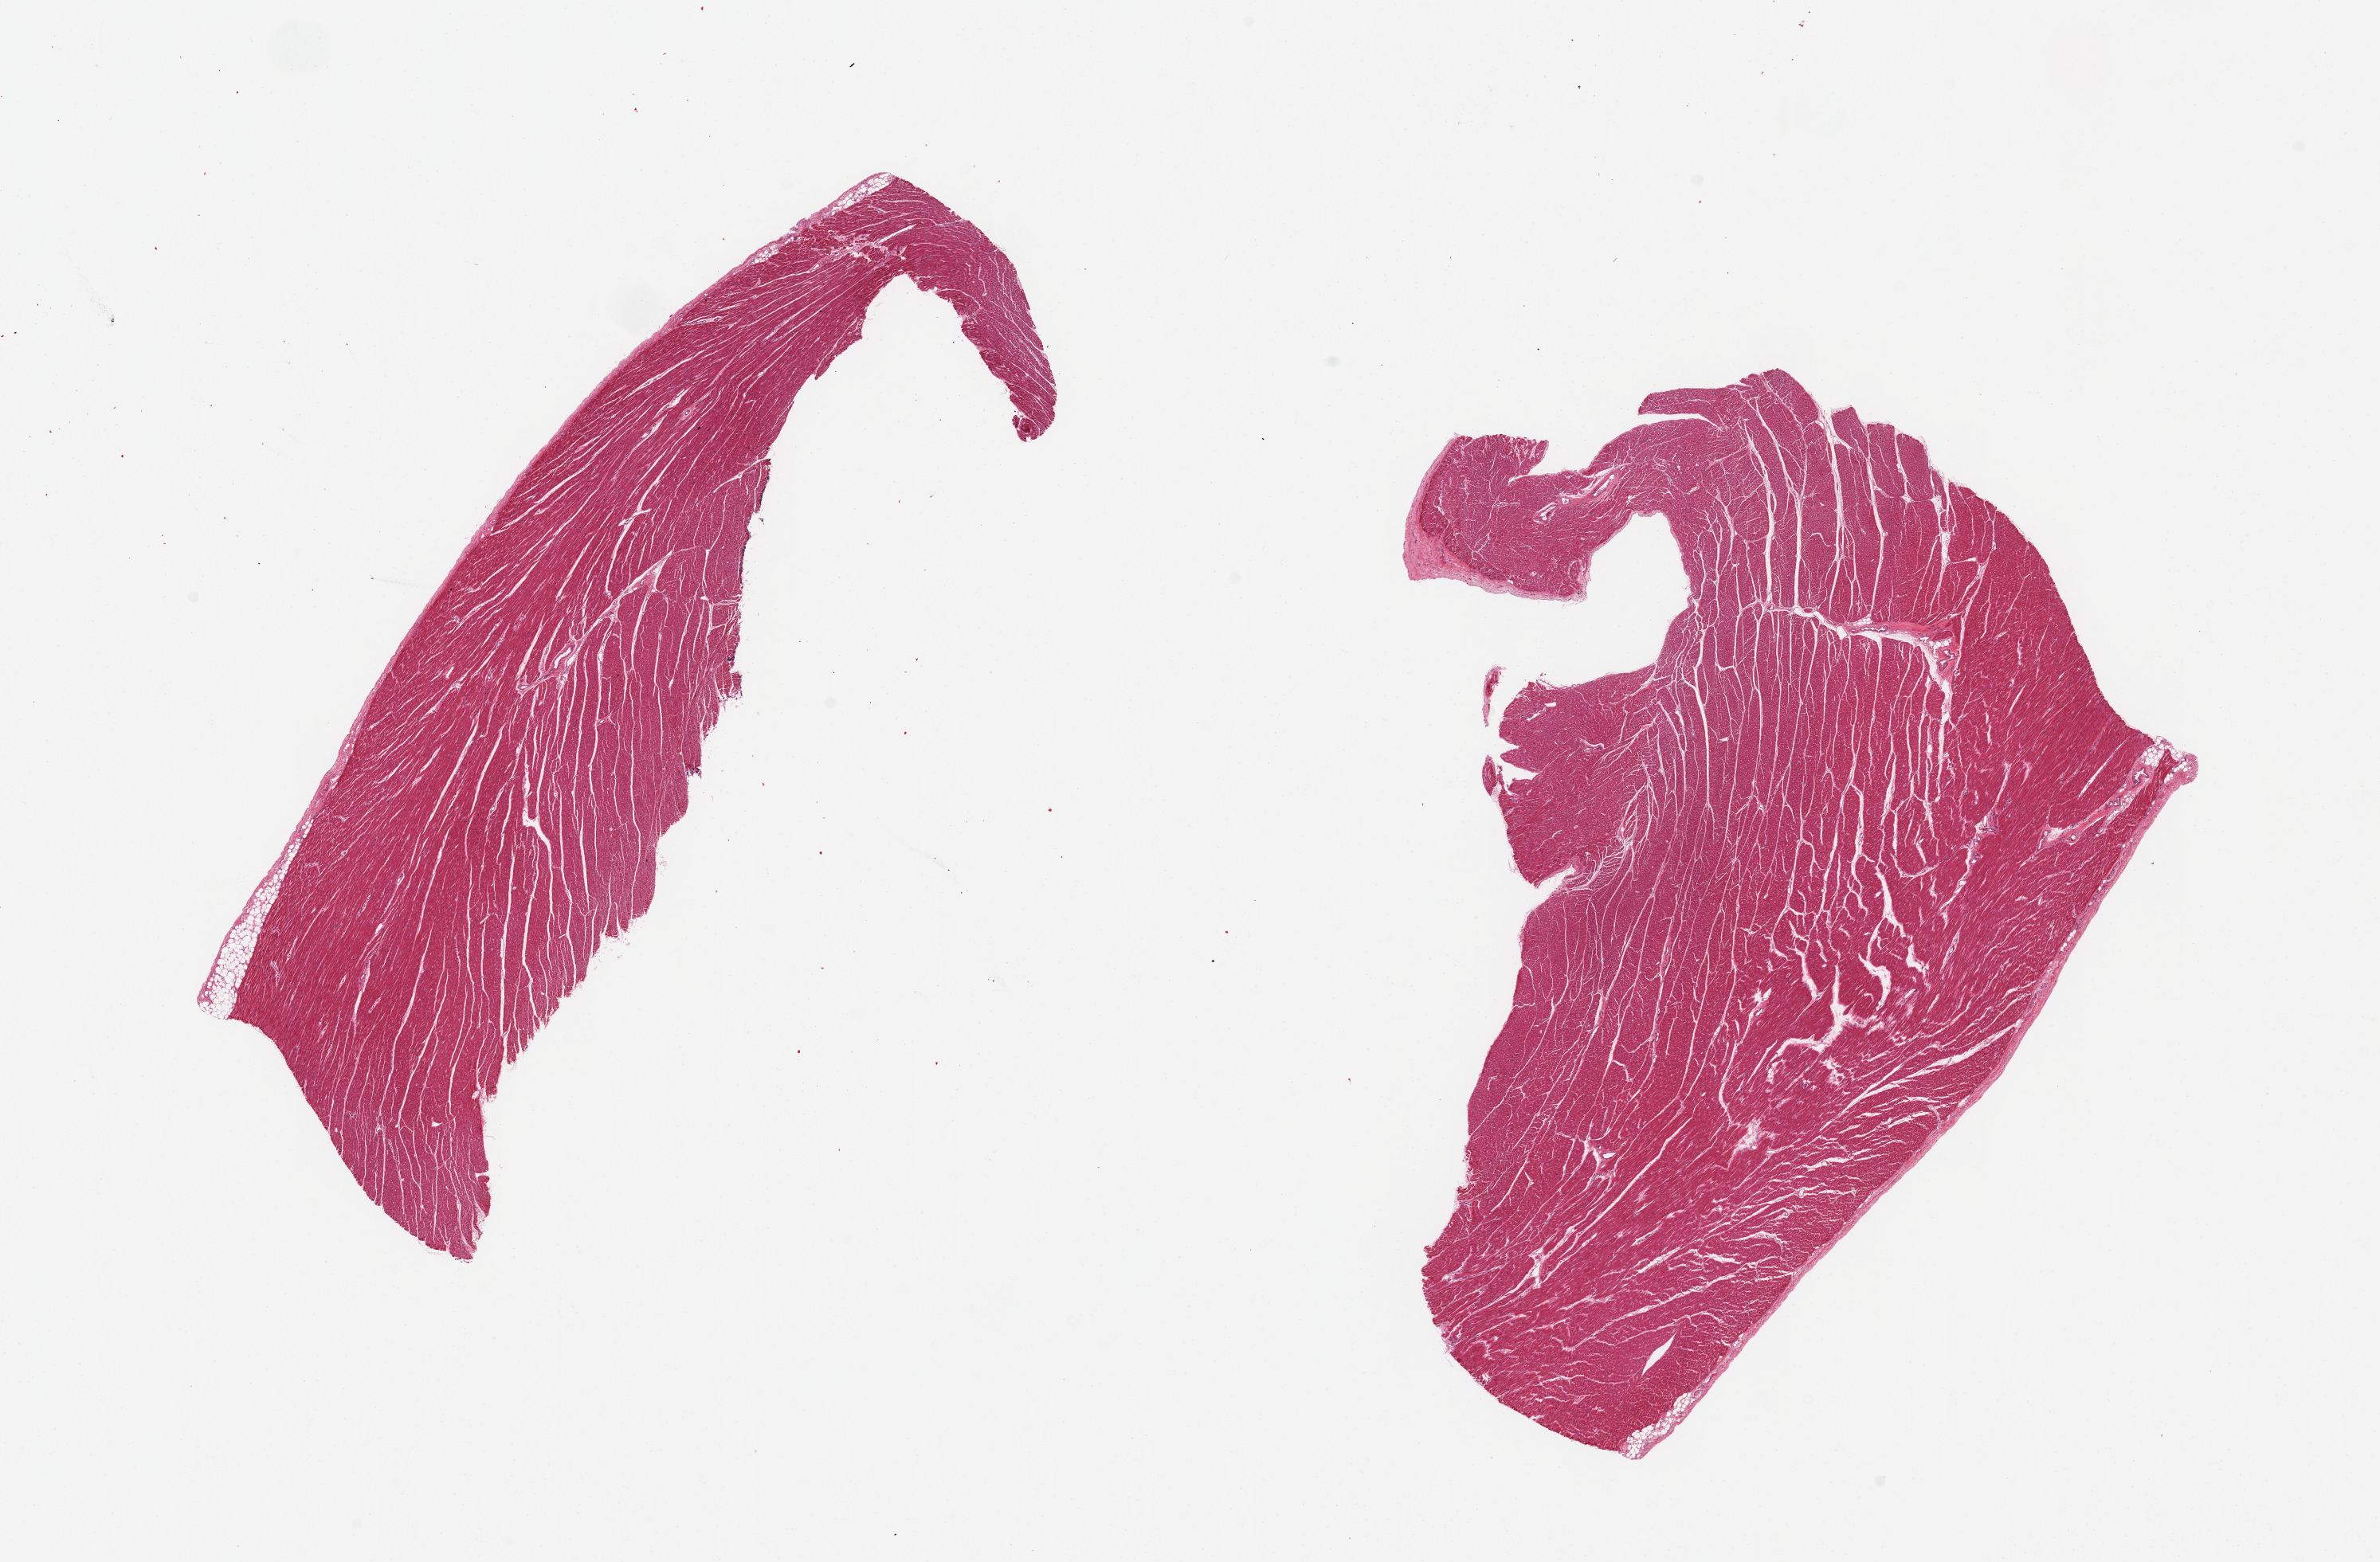
Digitized haematoxylin and eosin-stained section, shown as a low-resolution overview of the whole scanned area (about 23.6 x 15.5 mm, from a 20x scan). PAXgene-fixed paraffin-embedded (PFPE) section. Section of heart (target tissue). Donor tissue sample.
- pathologist's review note for this sample: 2 pieces, some lipofuscin pigment